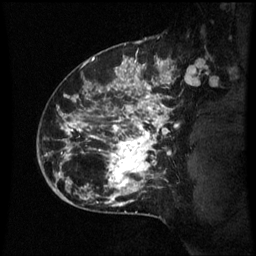
Breast MRI (dynamic contrast-enhanced), one sagittal slice; position 47 of 60 along the scan axis; dynamic contrast-enhanced series, image 2 of 3 at this slice position (ordered by acquisition); 1.5 T; TE 4.2 ms, TR 8.9 ms; 2.1 mm slice thickness; 256 × 256 image matrix. Patient: female, 42 years. Case-level facts recorded for this patient, not image findings: setting: breast cancer imaged before/during neoadjuvant chemotherapy; receptor status: HER2-positive.
Annotated regions visible in this slice (semi-automatically segmented with operator editing):
- analysis volume of interest (the breast-tissue region the enhancement analysis was run in; not a lesion): bounding box [x1, y1, x2, y2] px = [66, 82, 173, 193]
- tumour enhancement mask (voxels above the 70 % enhancement threshold inside the analysis volume of interest): [66, 82, 171, 191]